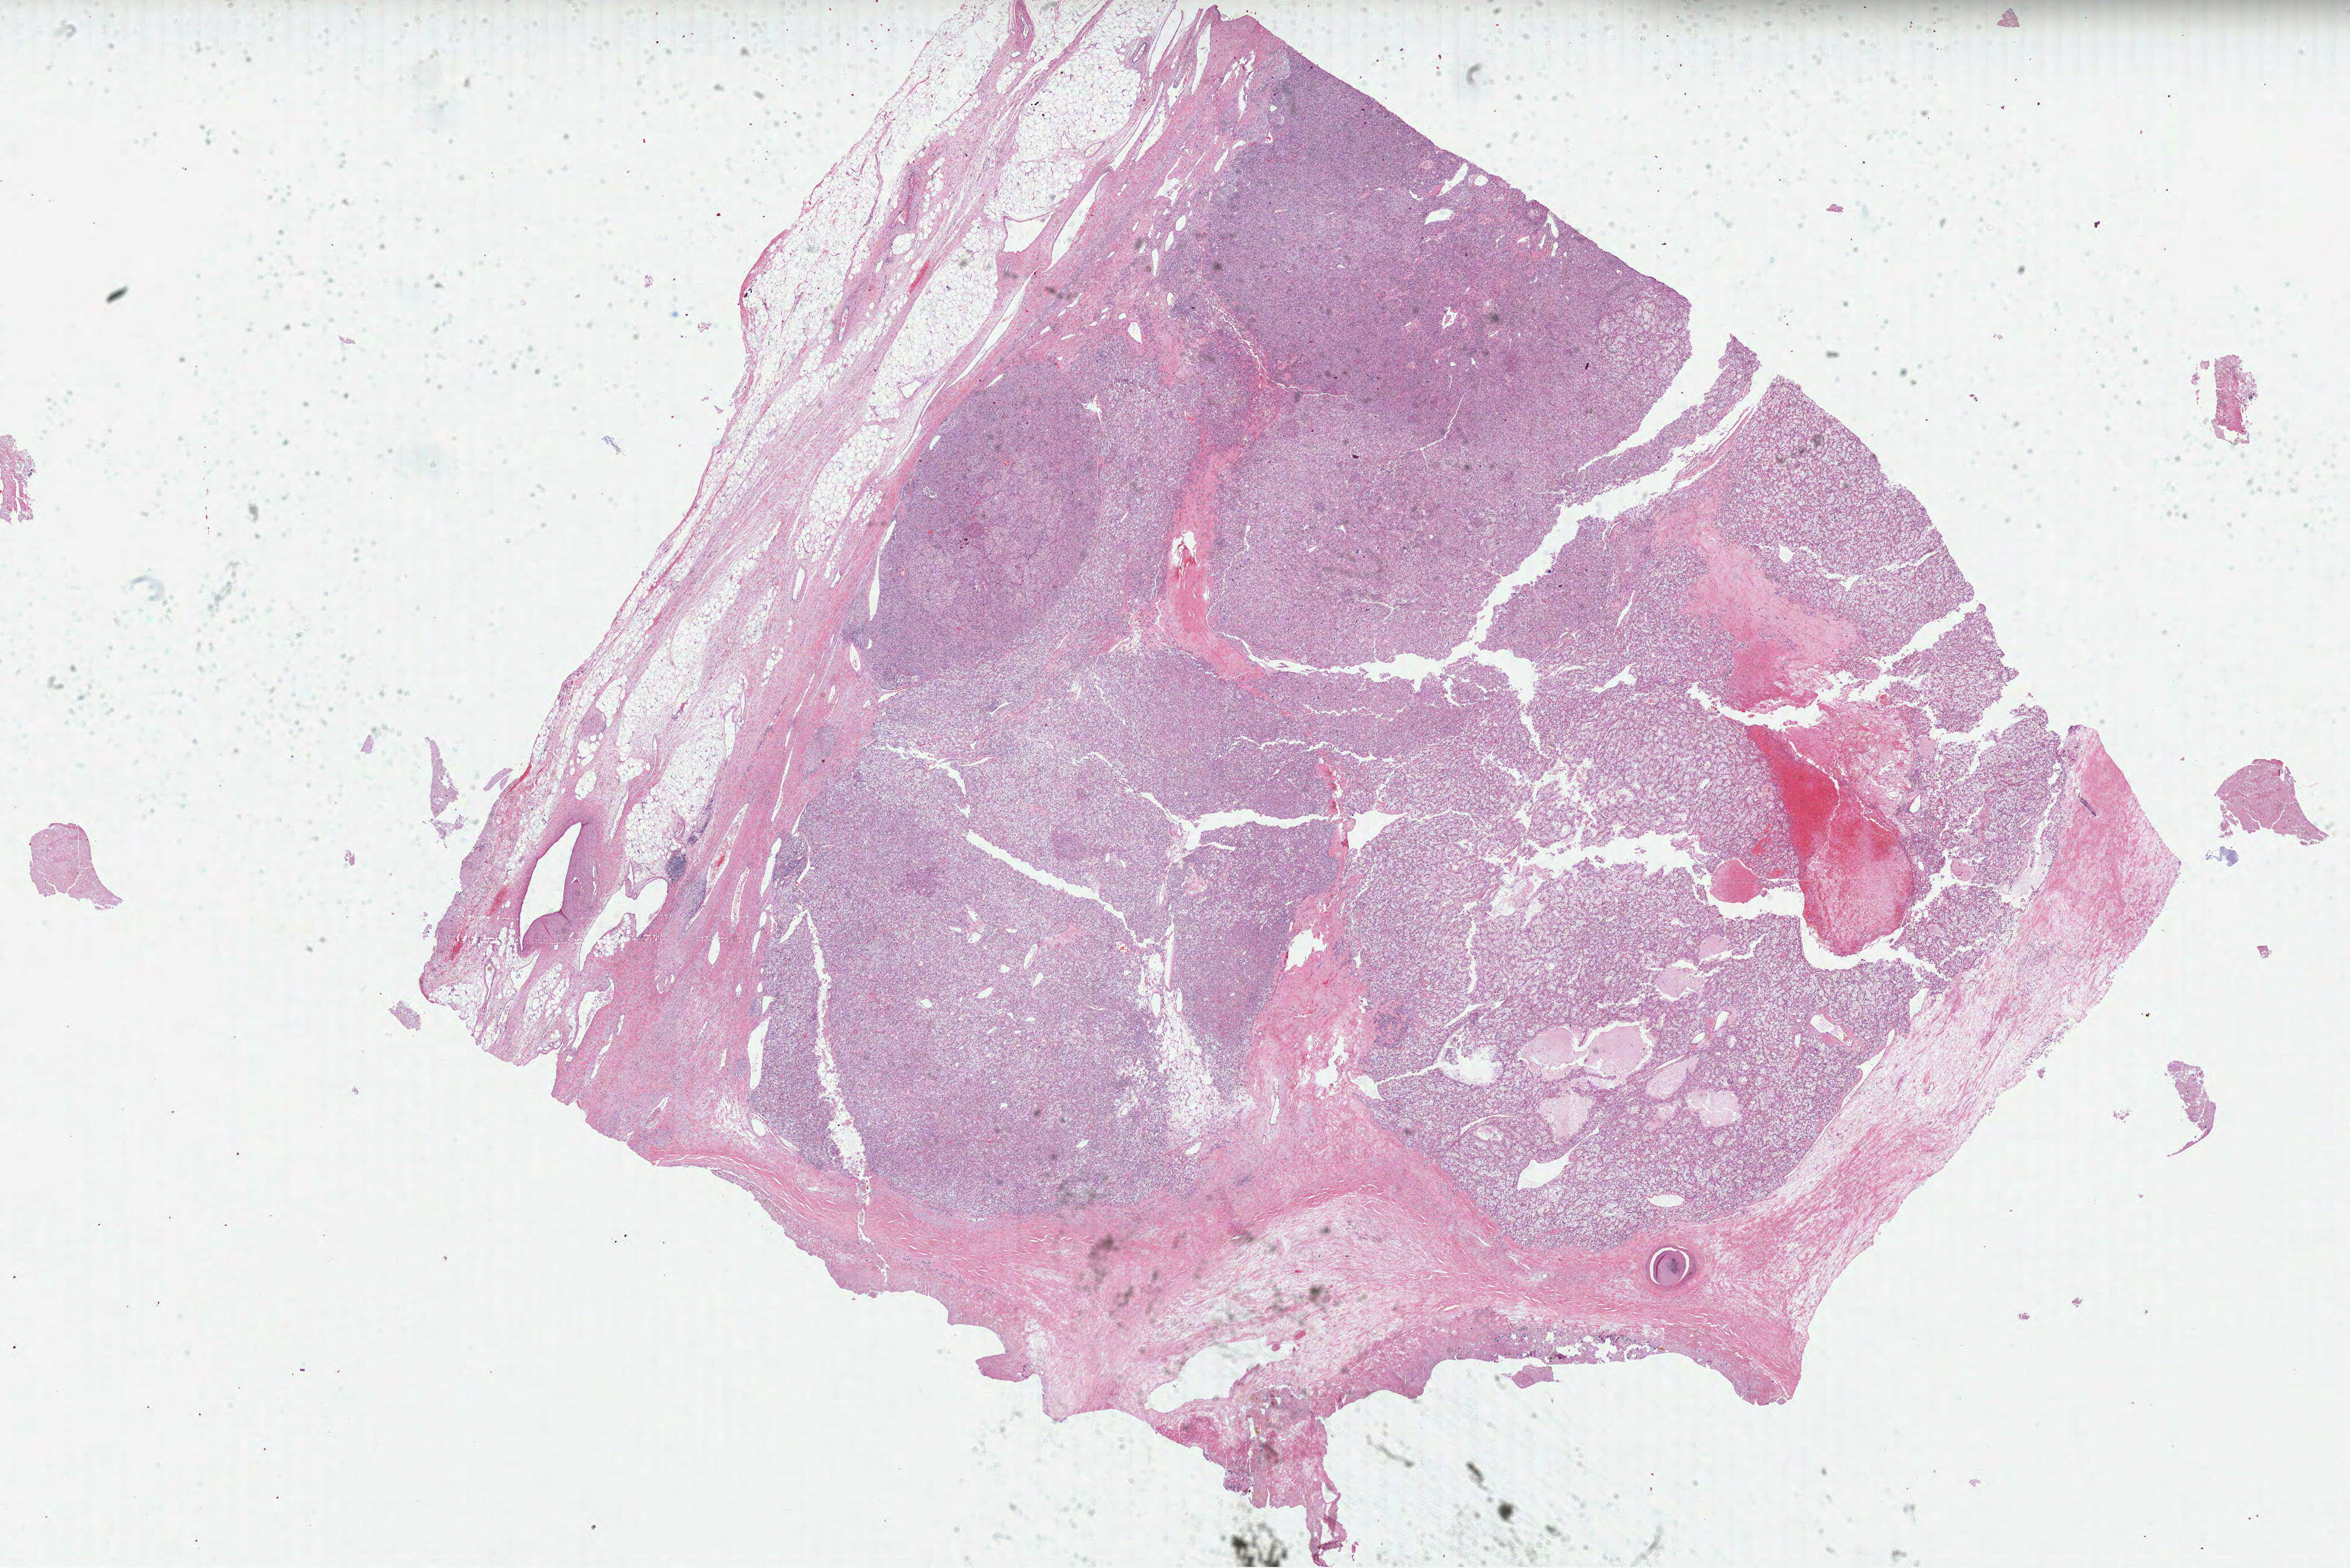
Whole-slide histology image, Hematoxylin and eosin (H&E) stained, shown as a low-resolution overview of the whole scanned area (about 31.2 x 20.8 mm, acquisition: 40x scan). FFPE section. Primary tumour sample from the kidney. Male patient; age at initial diagnosis 43 years. Histologic grade: G3 (poorly differentiated).
Laterality: left. Diagnosis: Clear cell adenocarcinoma, NOS. AJCC pathologic stage: IV.